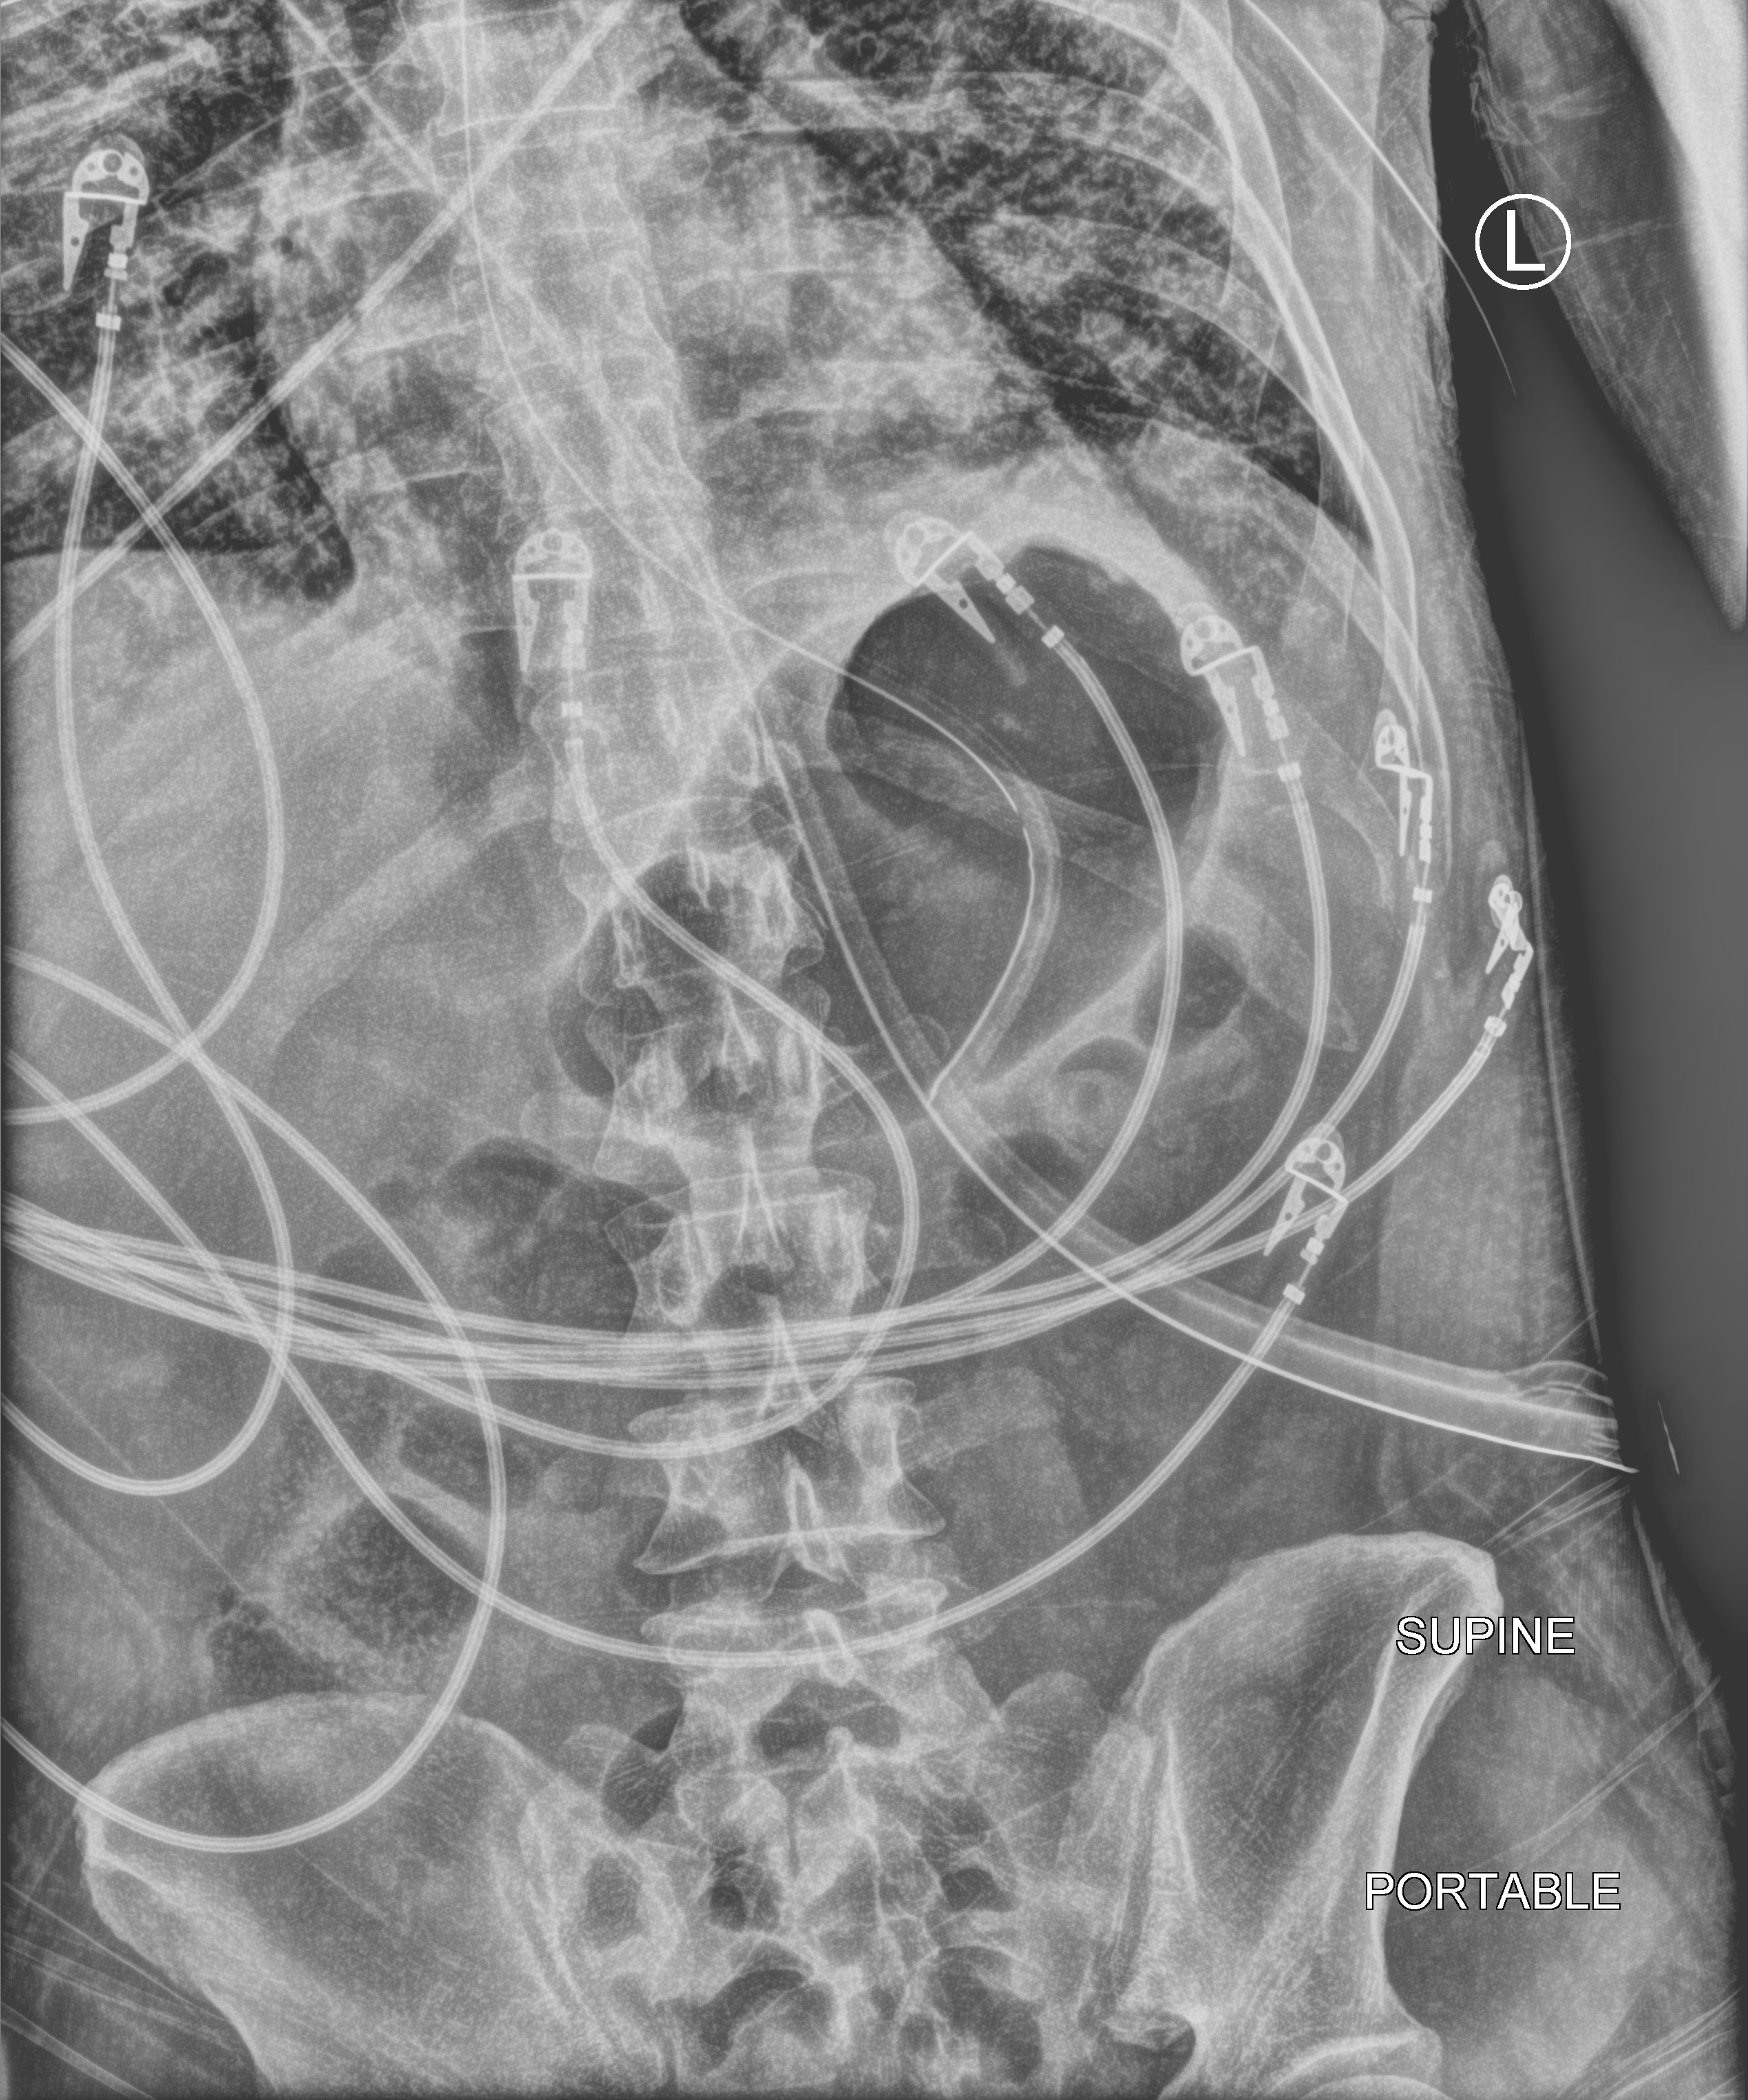
Portable abdomen radiograph; anteroposterior (AP) projection. Male patient hospitalised with COVID-19, age 18–59 years.
Admission-level facts for this patient (not findings on this image; timing relative to this image not recorded): admitted to intensive care during this hospital stay: yes.